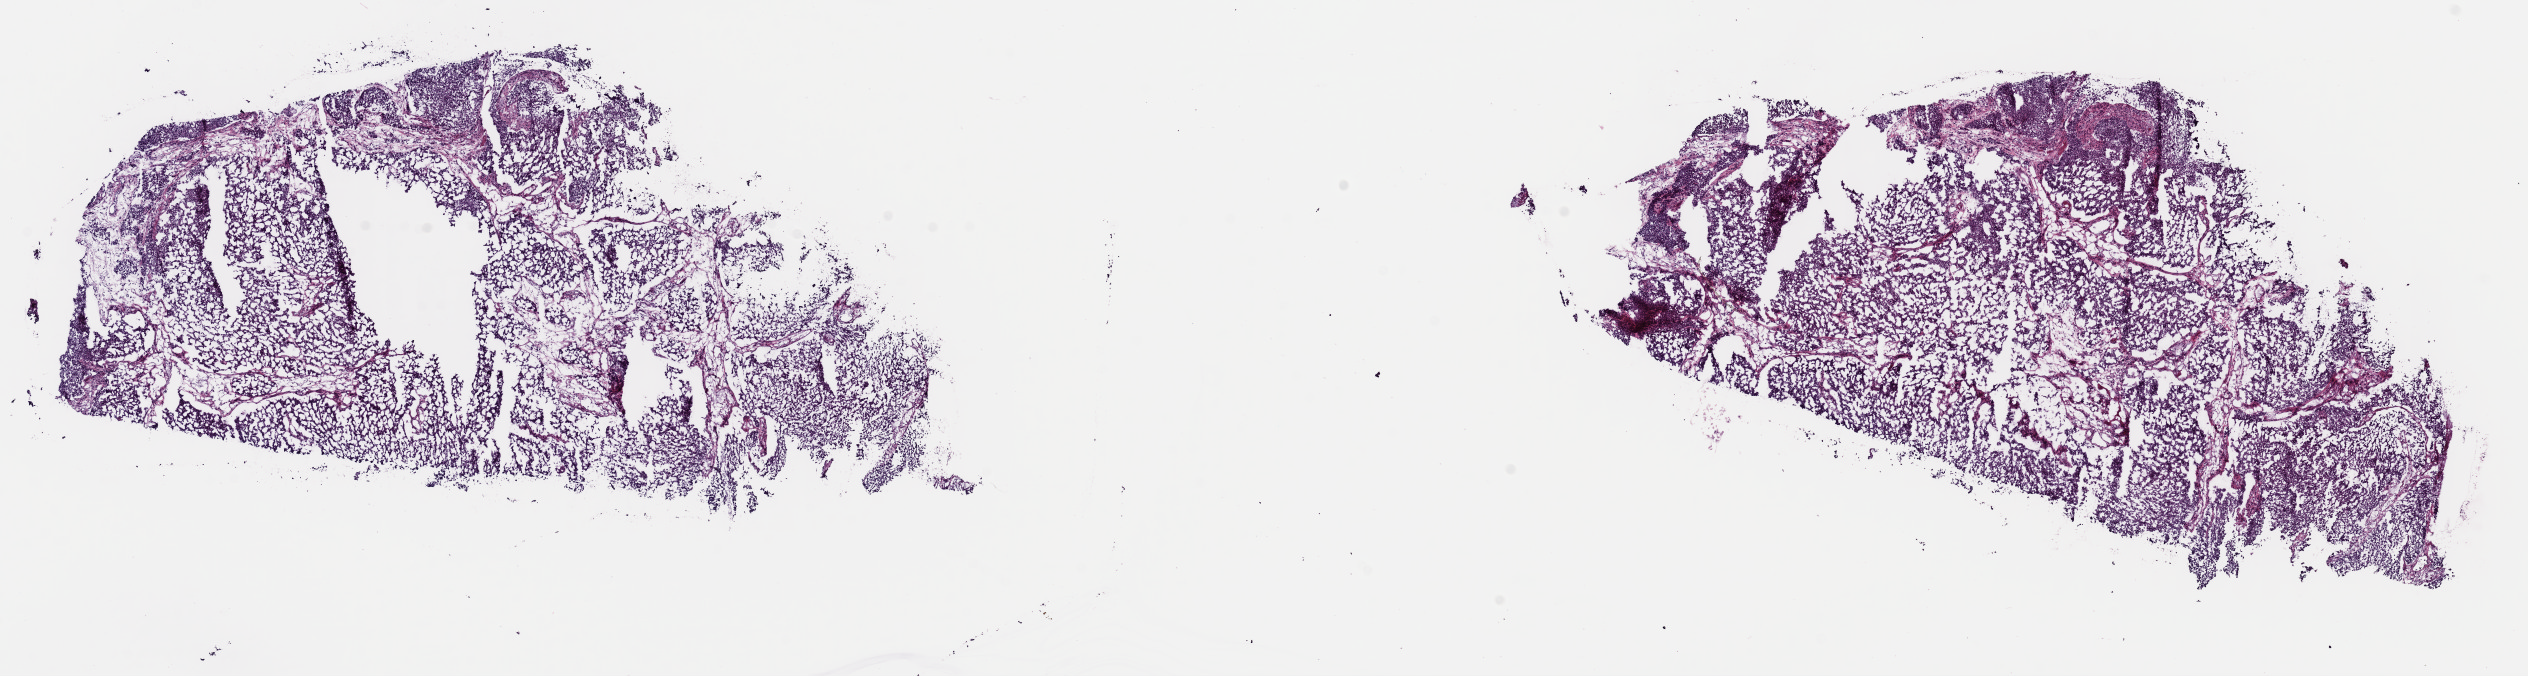
Whole-slide histology image, H&E, shown as a low-resolution overview of the whole scanned area (about 20.0 x 5.3 mm, acquisition: 40x scan); frozen section; sample: primary tumour, bladder. Female, age 81 years at initial diagnosis. Pathologist review of this section (percent, as recorded): tumour cells 100%, tumour nuclei 90%.
Pathologic diagnosis: Transitional cell carcinoma (trigone of bladder).